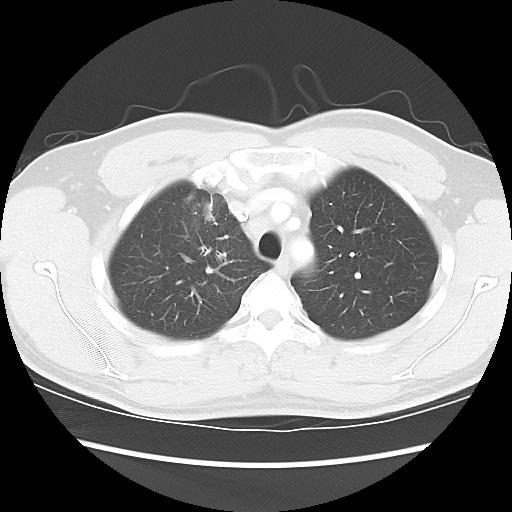
Chest CT, one axial slice; slice 68 of 80 in the series (ordered by position); reconstruction kernel LUNG; 120 kVp; lung window (W 1500 / L -600 HU); 512 × 512 image matrix, field of view 360 × 360 mm. Male patient, age 35 years. Case-level facts recorded for this patient, not image findings: clinical TNM (as recorded): T1c N1 M1b.
Outlined on this slice (rectangle marked by the reading radiologist):
- lung tumour (recorded histology: adenocarcinoma): box from (x=200, y=198) to (x=221, y=230) px